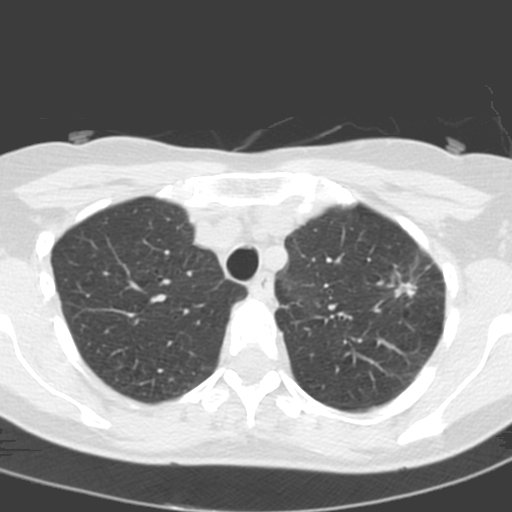
Low-dose screening chest CT, one axial slice; slice 153 of 193 in the series (ordered by position); lung window (W 1500 / L -600 HU); 512 × 512 image matrix, field of view 272 × 272 mm.
Outlined on this slice (manually delineated by an expert):
- lesion 1 (tumor, upper lobe of left lung): box from (x=395, y=282) to (x=416, y=297) px